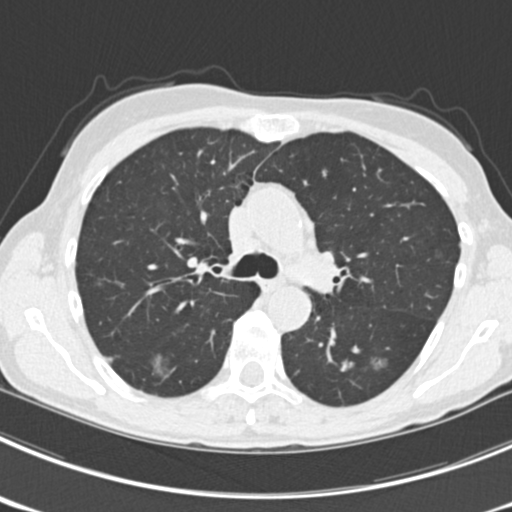
Axial slice from a low-dose chest CT screening exam. Third annual screen. Lung window (W 1500 / L -600 HU). 2 mm slice thickness. 512 × 512 image matrix. Female participant, aged 63 years at enrolment.
2 expert reader's lesion annotations on this slice (largest first), bounding box (x1, y1, x2, y2) in pixels: (141, 344, 180, 384); (356, 347, 398, 382). The screening reader recorded 9 non-calcified nodules or masses ≥4 mm on this exam; which of them these boxes mark is not recorded. Official screen result: positive, other. Lung cancer was diagnosed 15 days after this screen: bronchiolo-alveolar adenocarcinoma, NOS, right upper lobe, right middle lobe, right lower lobe, left upper lobe, left lower lobe, moderately differentiated (G2), stage IV (AJCC 6th edition).